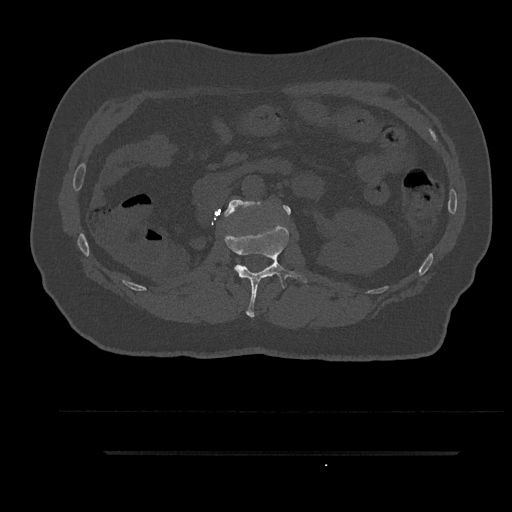
CT including the spine, one axial slice; slice 161 of 797 in the series (ordered by position); reconstruction kernel Br40s/3; 120 kVp; bone window (W 1800 / L 400 HU); 0.5 mm slice thickness; 512 × 512 image matrix, field of view 432 × 432 mm. Male patient, age 63 years. Case-level facts recorded for this patient, not image findings: primary cancer: renal; vertebrae with lytic lesions (as recorded): T8.
Annotated regions visible in this slice (semi-automatic segmentation, software-assisted and operator-edited):
- L1 vertebra: bounding box (x1, y1, x2, y2) in pixels: (225, 225, 307, 318)
- L2 vertebra: (224, 199, 291, 217)